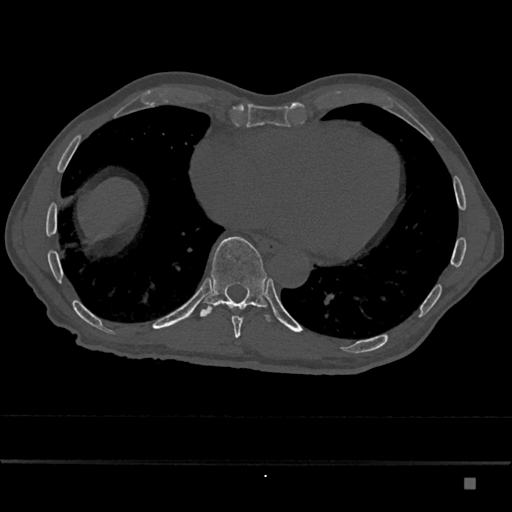
CT including the spine, one axial slice; position 765 of 797 along the scan axis; 120 kVp; bone window (W 1800 / L 400 HU); 512 × 512 image matrix, field of view 390 × 390 mm. Male patient, age 72 years. Case-level facts recorded for this patient, not image findings: primary cancer: prostate.
Annotated regions visible in this slice (semi-automatic segmentation, software-assisted and operator-edited):
- T10 vertebra: bounding box [x1, y1, x2, y2] px = [200, 237, 272, 321]
- T9 vertebra: [232, 308, 245, 338]